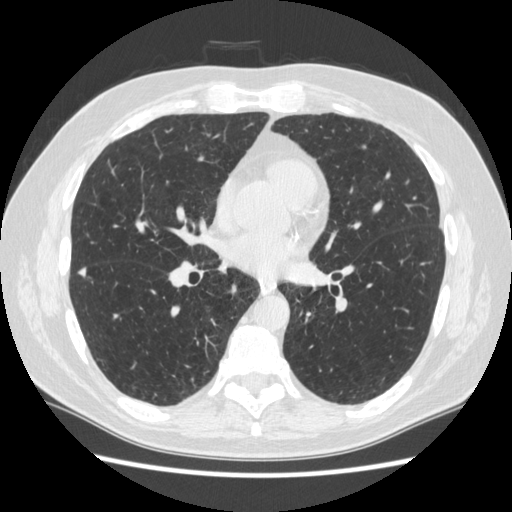
Low-dose screening chest CT, one axial slice; slice 127 of 267 in the series (ordered by position); reconstruction kernel STANDARD; lung window (W 1500 / L -600 HU); 512 × 512 image matrix, field of view 360 × 360 mm.
Outlined on this slice (manually delineated by an expert):
- lesion 2 (nodule, lower lobe of right lung): box from (x=79, y=268) to (x=85, y=276) px